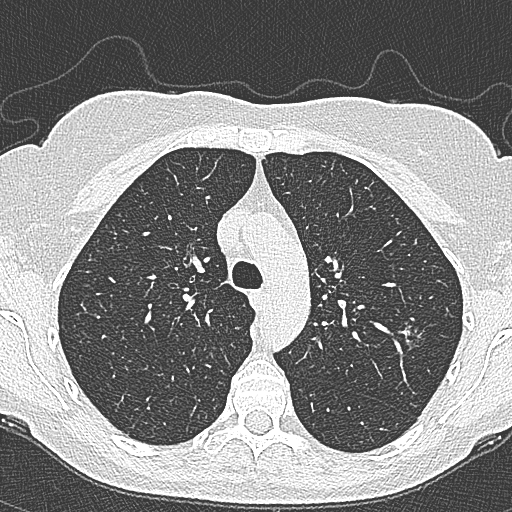
Chest CT (low-dose screening protocol), one axial image. Second annual screen. Lung window (W 1500 / L -600 HU). 1 mm slice thickness. Lung (sharp) reconstruction kernel (B80f). Female, age 65 years at enrolment.
• Lesion marked by an expert reader, bounding box (x1, y1, x2, y2) in pixels: (391, 309, 436, 354).
• The screening reader recorded 4 non-calcified nodules or masses ≥4 mm on this exam; which of them this box marks is not recorded.
• Official screen result: positive, change unspecified: nodule(s) >= 4 mm or enlarging nodule(s), mass(es), or other non-specific abnormalities suspicious for lung cancer.
• Participant outcome: lung cancer diagnosed 54 days after this screen — bronchiolo-alveolar carcinoma, non-mucinous, left upper lobe, stage IA (AJCC 6th edition), 10 mm at pathology.